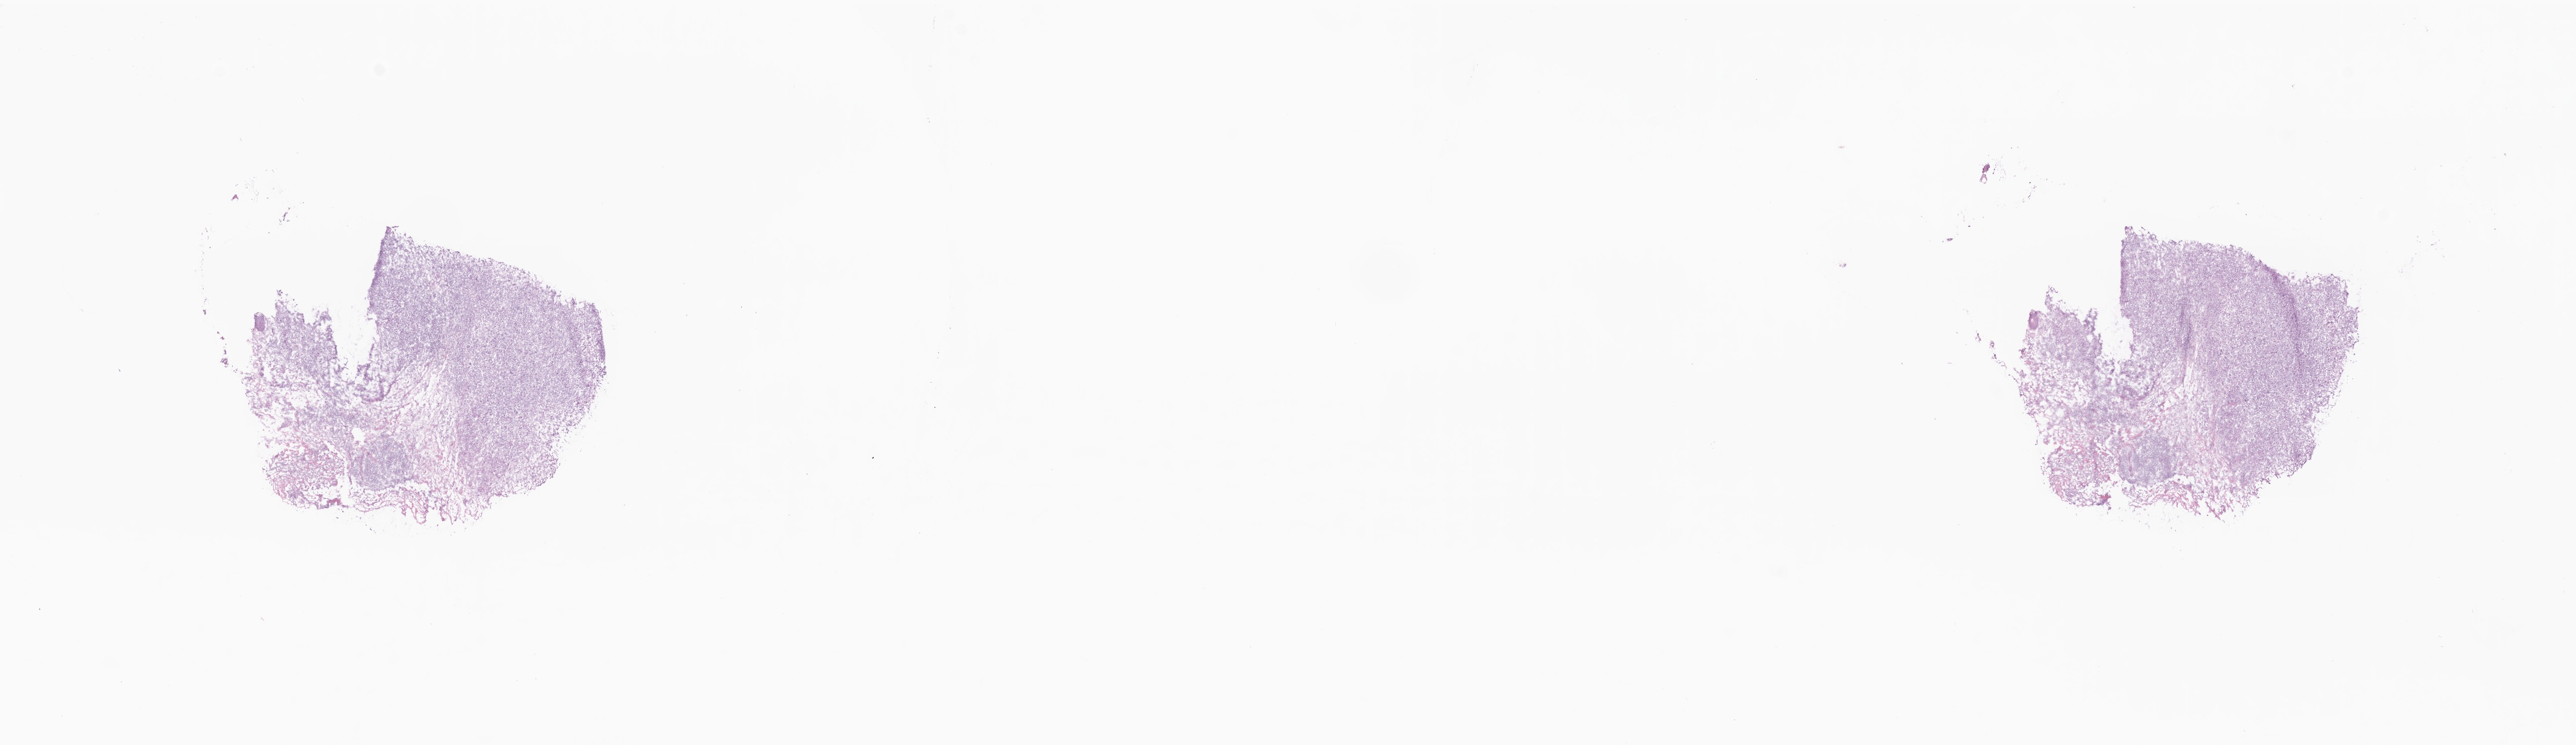
Digitized hematoxylin and eosin (H&E)-stained section, whole scanned area (about 21.8 x 6.3 mm) shown as a low-resolution overview; frozen section (tissue freezing medium); metastatic tumor tissue, resected from skin. Male, age 75 years at initial diagnosis. Pathologist review of this section (percent, as recorded): tumor cells 80%, tumor nuclei 90%, stromal cells 0%, necrosis 20%, normal cells 0%. Infiltration values recorded for this section: lymphocyte infiltration 0%, monocyte infiltration 0%, neutrophil infiltration 0%.
* section: bottom of the tissue portion
* patient diagnosis (primary): Malignant melanoma, NOS